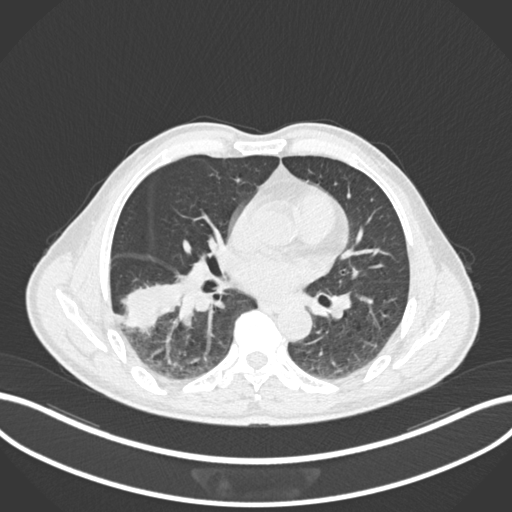
Chest CT, one axial slice; slice 95 of 208 in the series (ordered by position); reconstruction kernel B30f; lung window (W 1500 / L -600 HU); 512 × 512 image matrix, field of view 400 × 400 mm. Patient: male, 58 years. Case-level facts recorded for this patient, not image findings: clinical TNM (as recorded): T3 N0 M0; histopathological grade: G2.
Outlined on this slice (rectangle marked by the reading radiologist):
- lung tumour (recorded histology: squamous cell carcinoma): box from (x=119, y=270) to (x=180, y=338) px